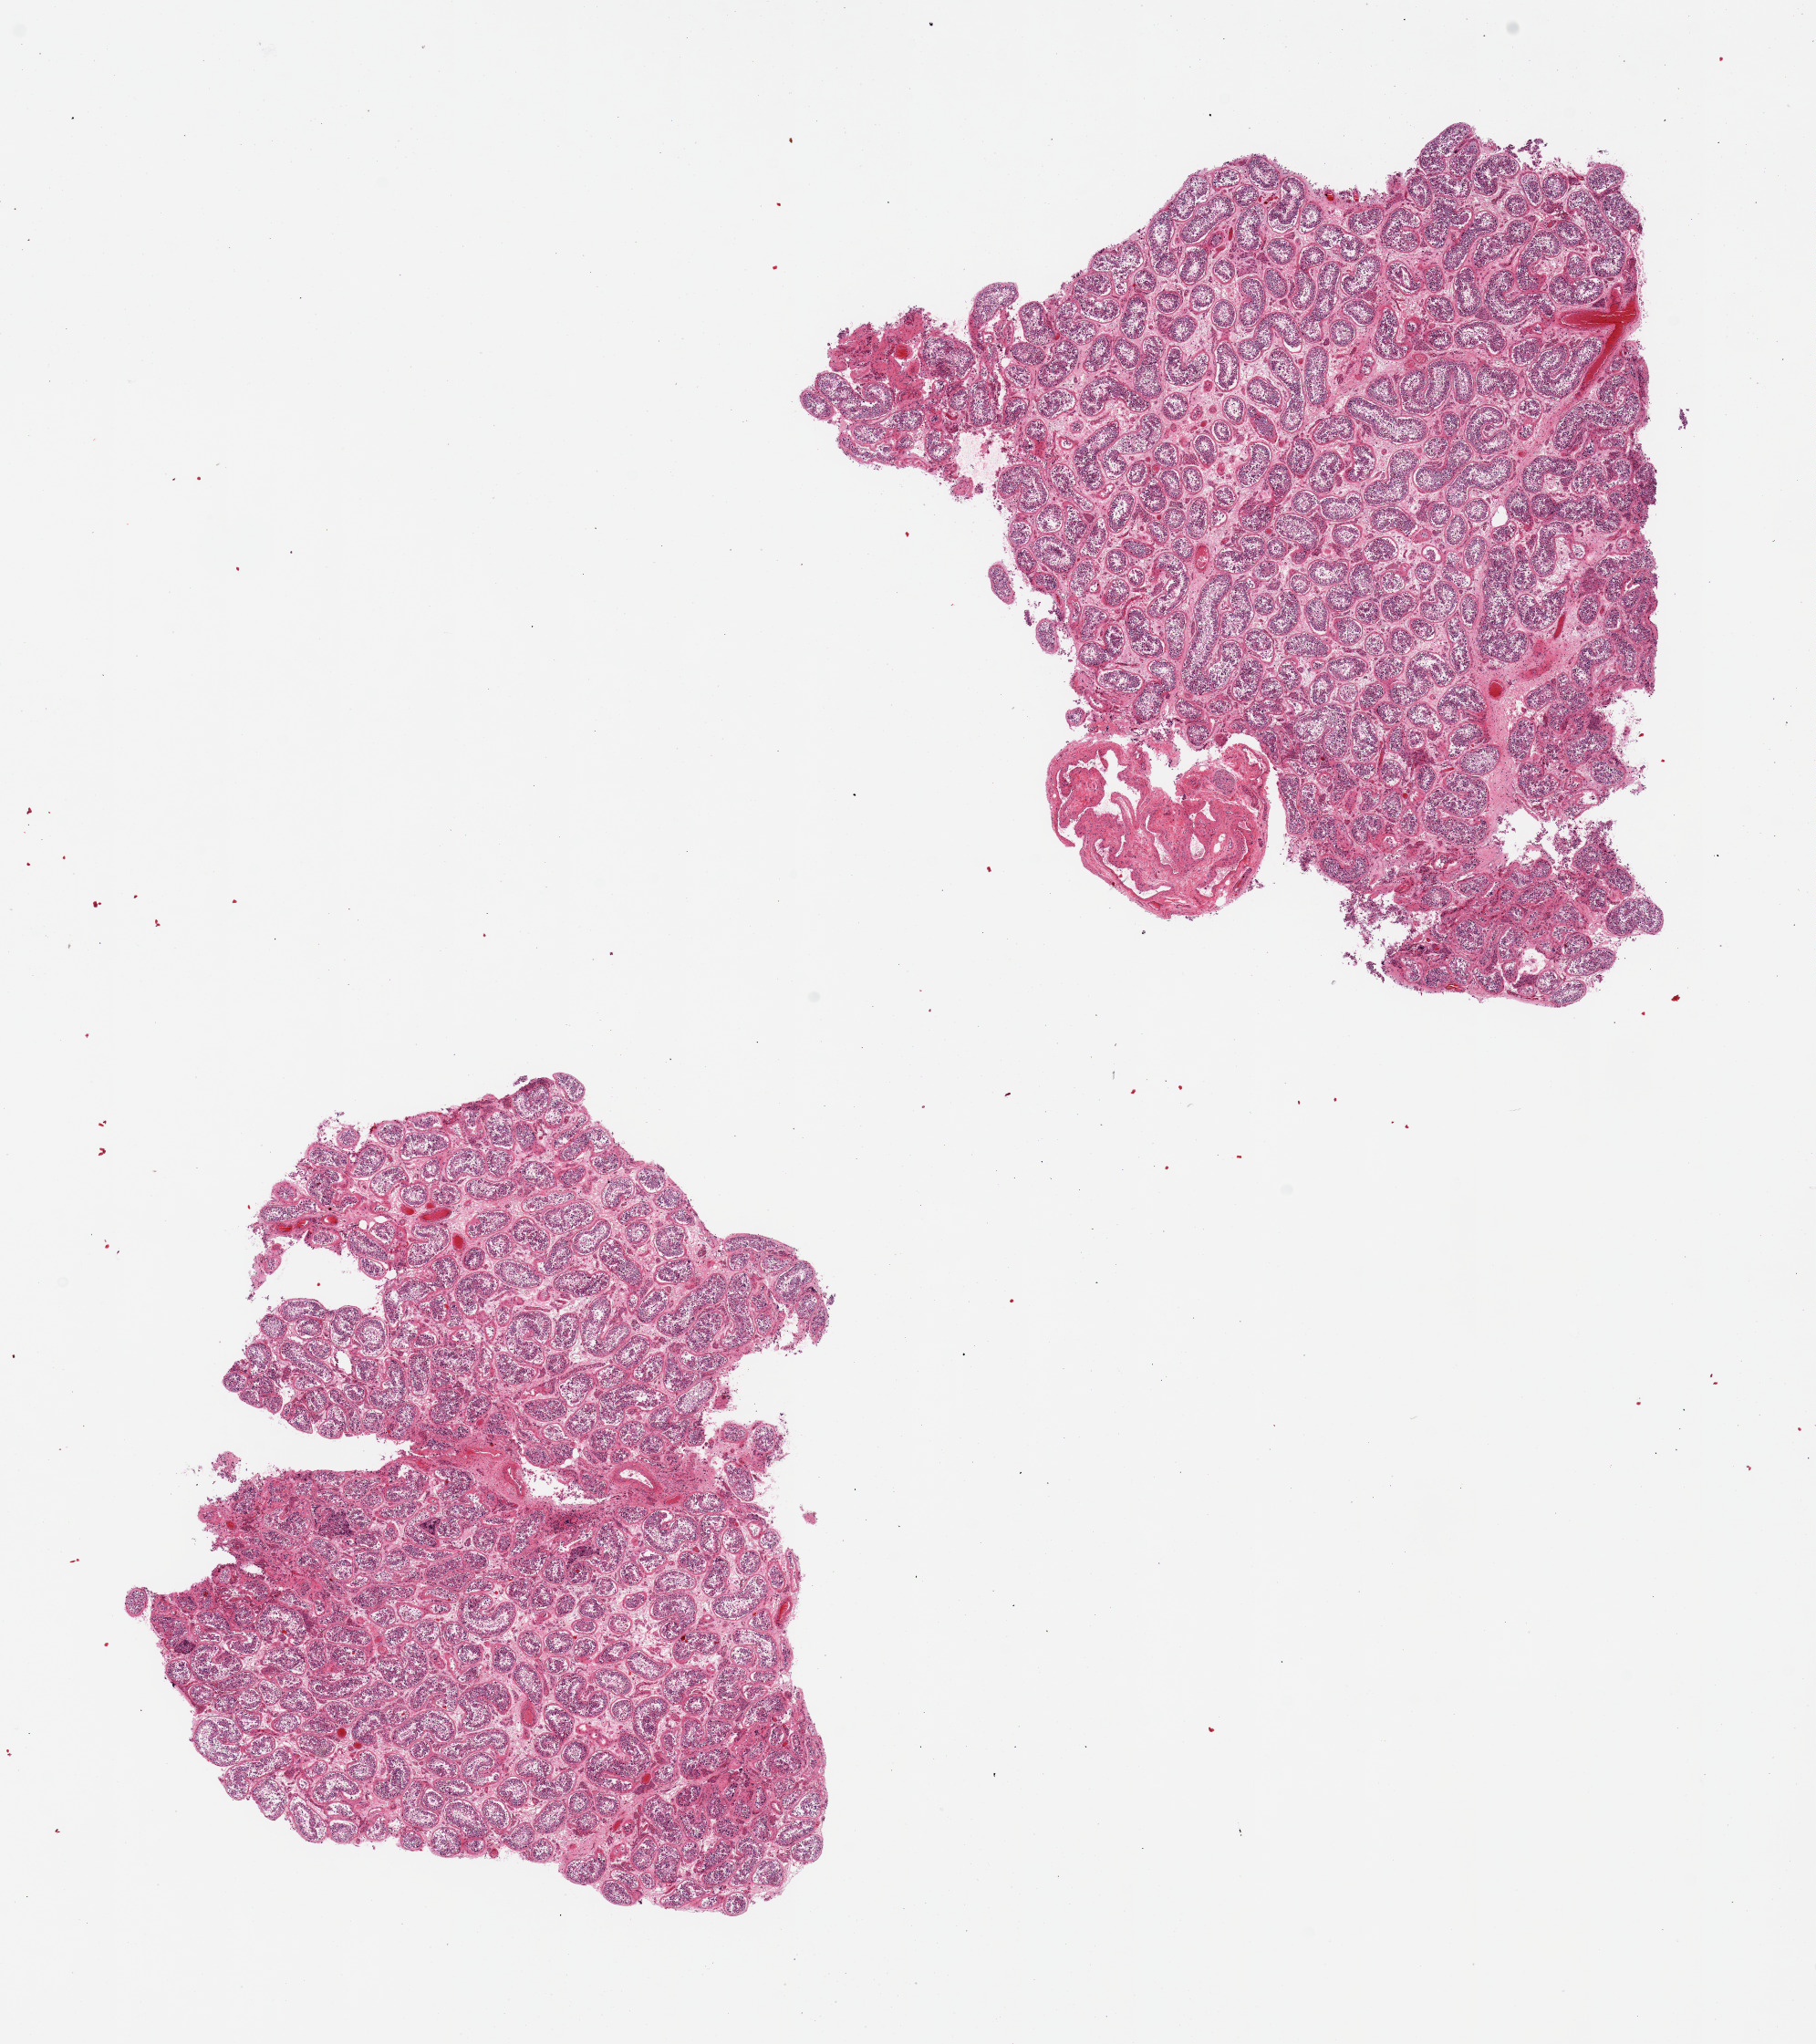
Whole-slide image, haematoxylin and eosin stain, low-resolution overview of the scanned area, about 15.8 x 17.7 mm (from a 20x scan); PAXgene-fixed, paraffin-embedded tissue; section of testis (target tissue); donor tissue sample. Male donor.
Reviewer comment on this tissue sample: 2 pieces. spermatogenesis. 2mm vascular plexus at one edge.